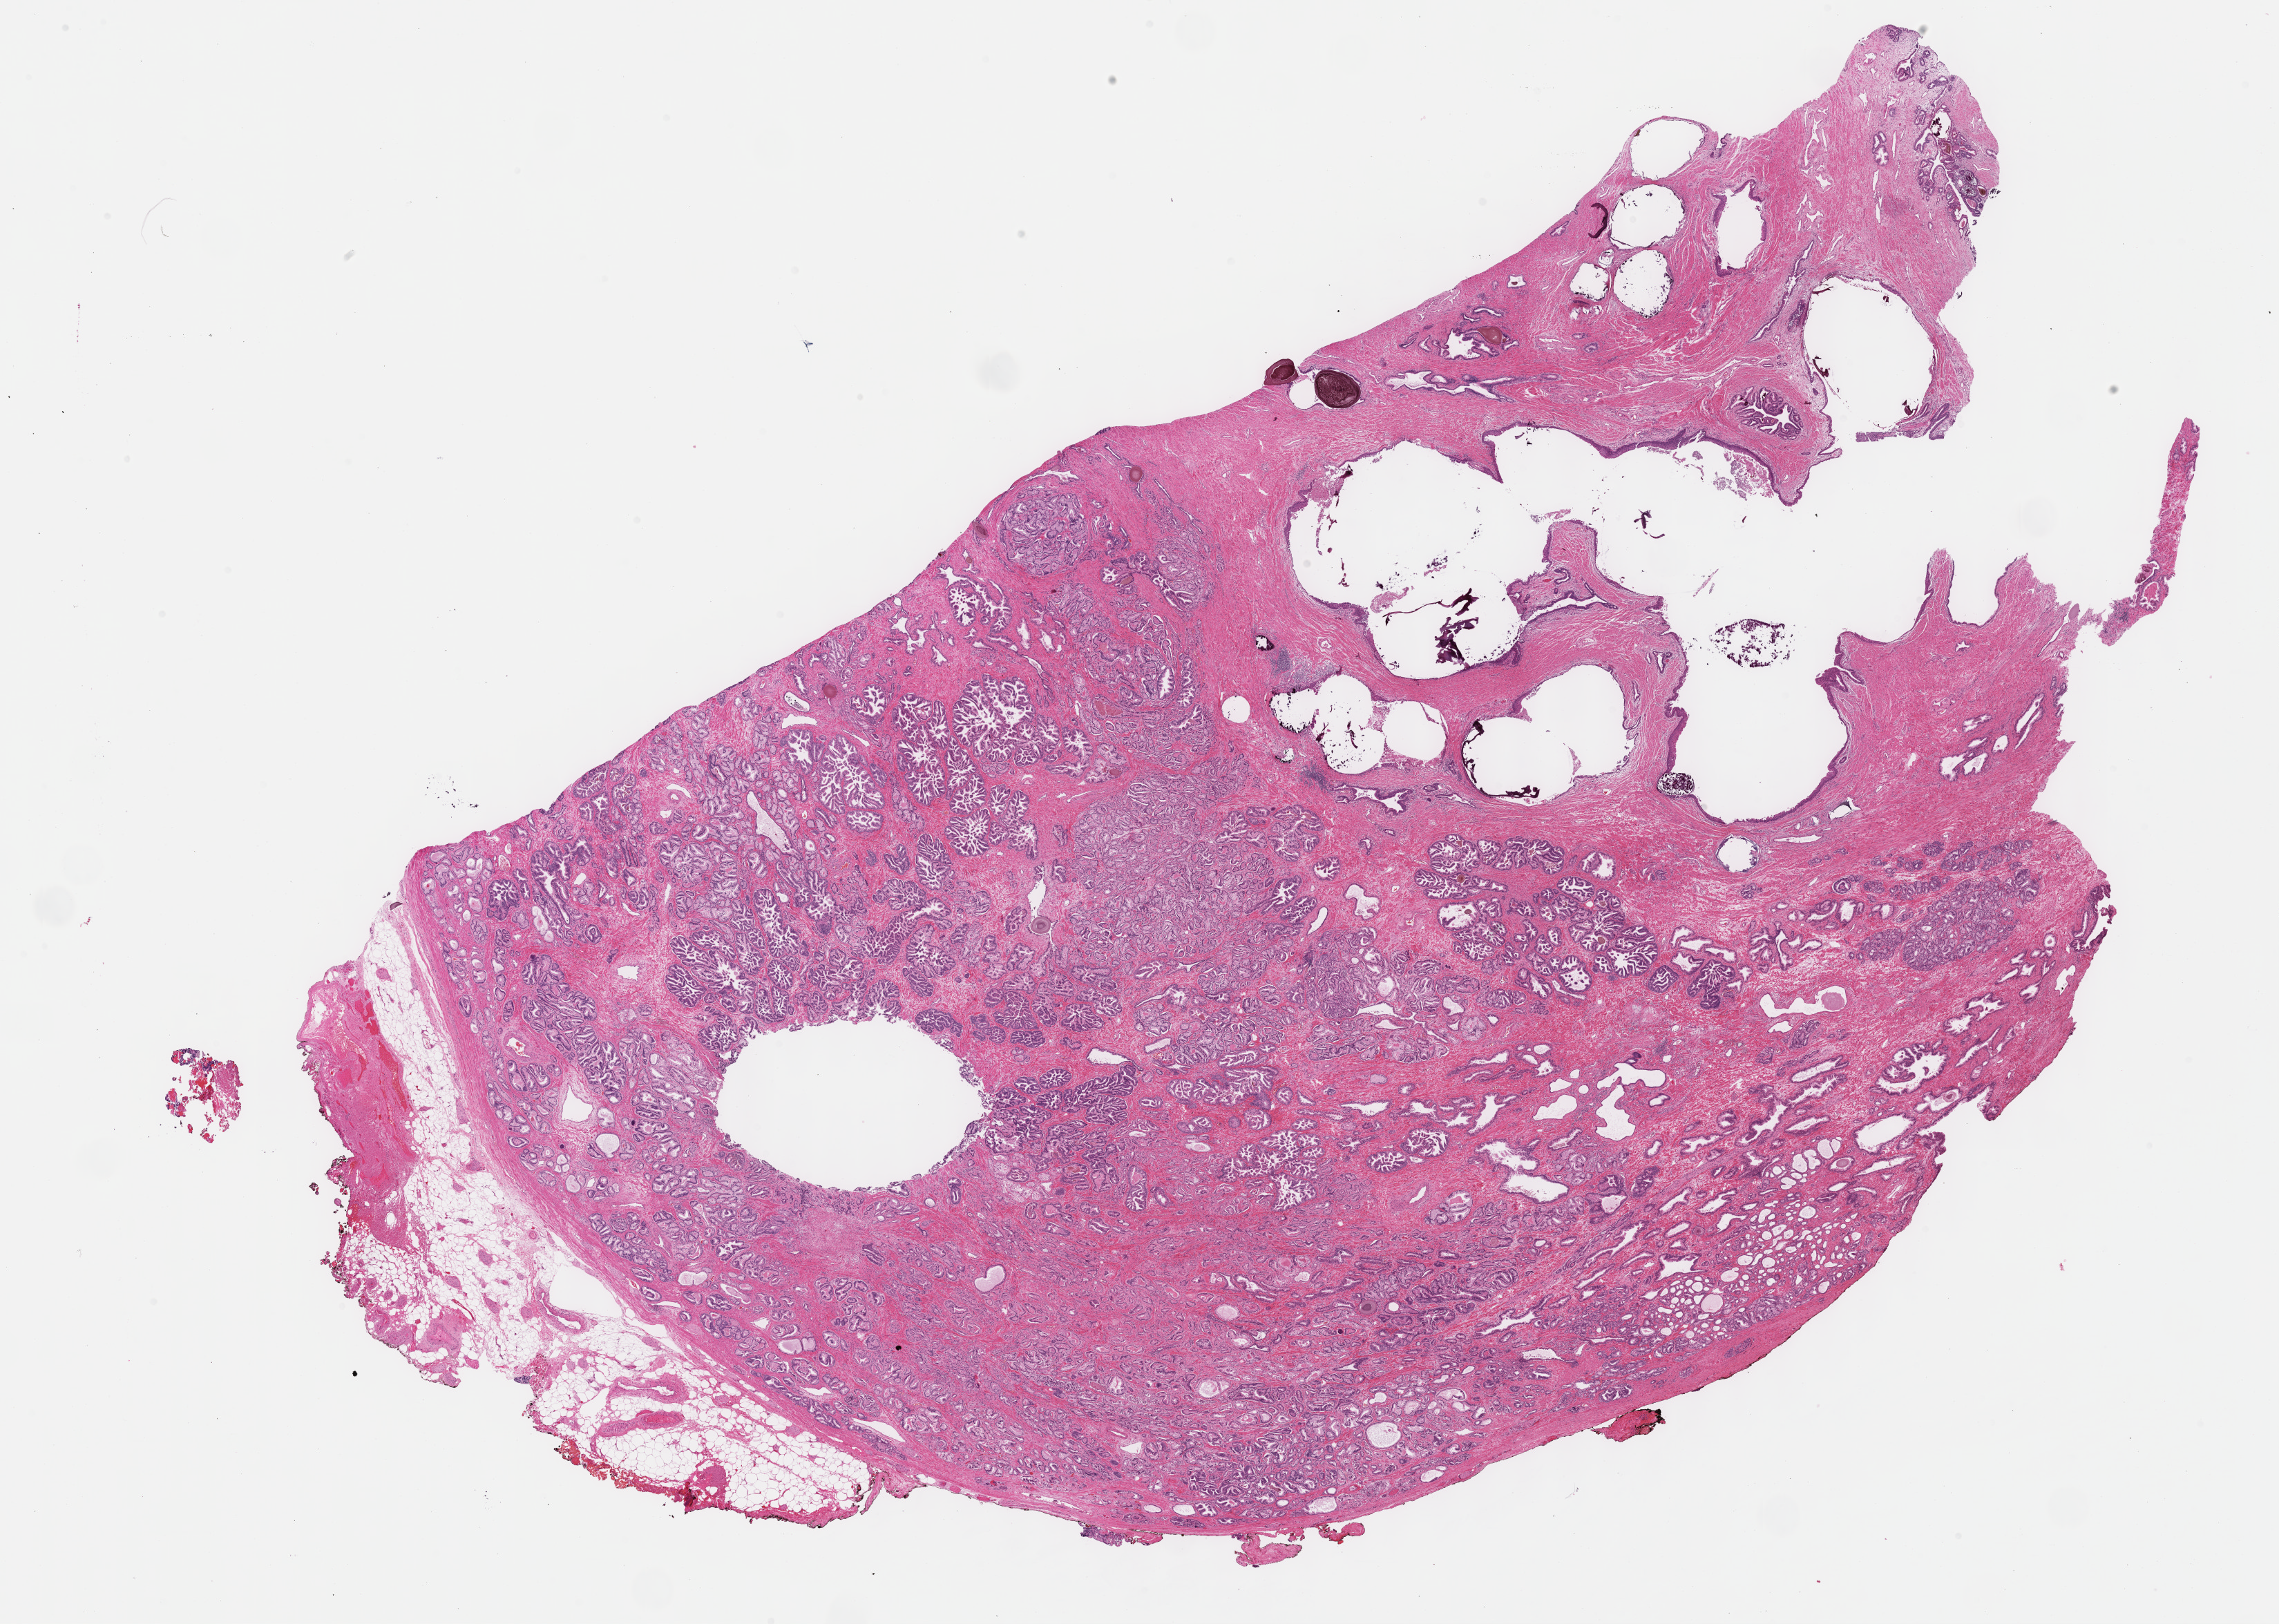
Whole-slide histology image, H&E-stained, a low-resolution overview of the entire scanned area, about 26.7 x 19.0 mm (acquisition: 40x scan). Formalin-fixed paraffin-embedded (FFPE) diagnostic section. Sample: primary tumour, prostate. Male patient; age at initial diagnosis 67 years. Gleason score: 7 (3+4).
• lymph nodes positive (case pathology): 0 of 7 examined
• diagnosis: Adenocarcinoma, NOS (prostate gland)